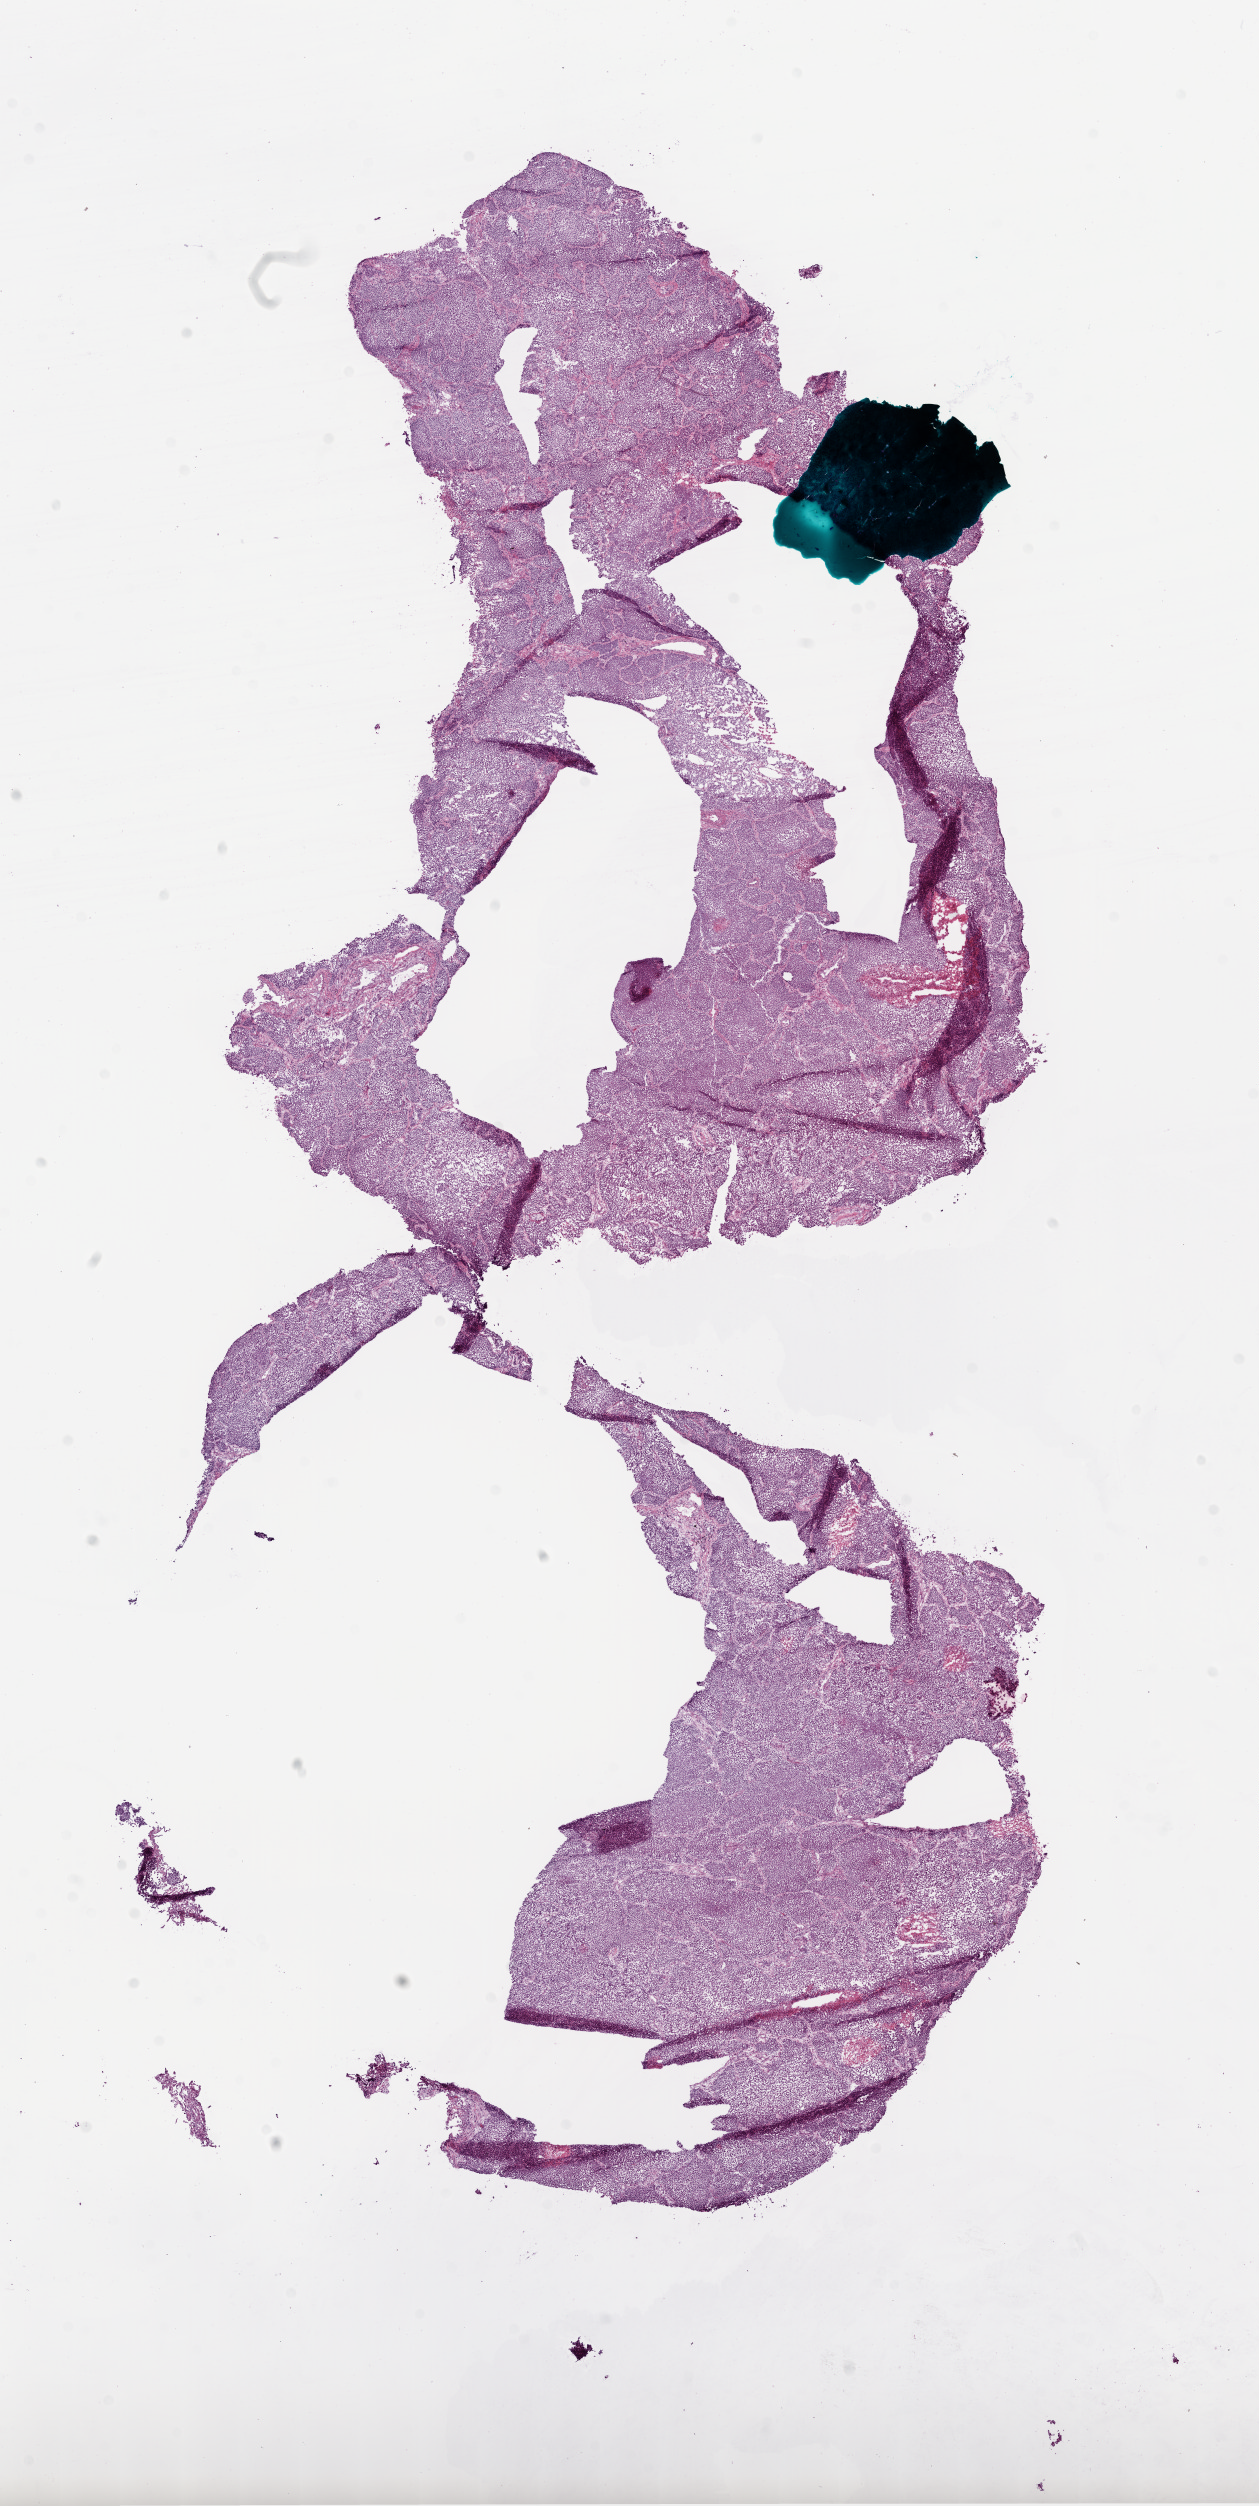
Whole-slide histology image, H&E-stained — shown as a low-resolution overview of the whole scanned area (about 10.2 x 20.2 mm), frozen section from the bottom of the tissue portion, sample: primary tumour, lung. Male patient; age at initial diagnosis 77 years. Slide review estimates, as recorded: tumour nuclei 99%, necrosis 0%.
* AJCC pathologic stage: IB
* diagnosis: Squamous cell carcinoma, NOS (lower lobe, lung)